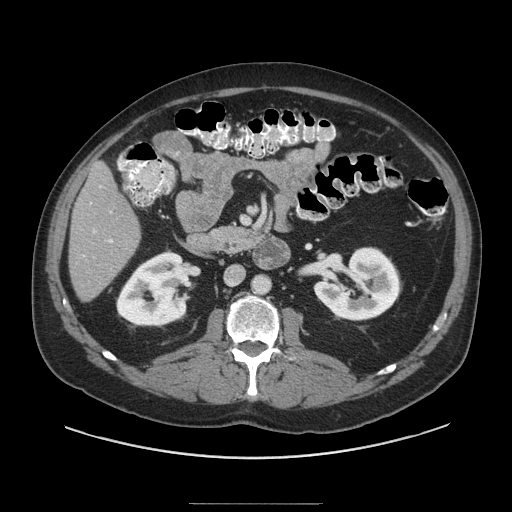
Contrast-enhanced abdominal CT (liver protocol), one axial slice; slice 33 of 91 in the series (ordered by position); reconstruction kernel STANDARD; soft-tissue window (W 400 / L 40 HU); 512 × 512 image matrix, field of view 440 × 440 mm. Case-level facts recorded for this patient, not image findings: diagnosis: hepatocellular carcinoma (patient treated with transarterial chemoembolisation; whether this scan precedes or follows treatment is not stated here); TNM stage (as recorded): Stage-I; Child-Pugh class: A; tumour differentiation: well differentiated; tumour nodularity: uninodular.
Structures marked on this image (semi-automatically segmented with operator editing):
- liver parenchyma outside the tumour (the mass and vessels are separate outlines, so this box may not span the whole liver): bounding box [x1, y1, x2, y2] px = [68, 162, 140, 300]
- liver vessels: [83, 186, 113, 256]